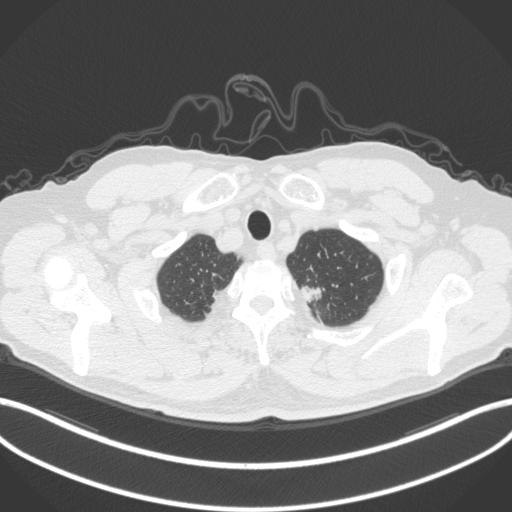
Chest CT, one axial slice; slice 349 of 382 in the series (ordered by position); reconstruction kernel B31f; lung window (W 1500 / L -600 HU); 1 mm slice thickness; 512 × 512 image matrix, field of view 400 × 400 mm. Patient: male, 64 years. Case-level facts recorded for this patient, not image findings: clinical TNM (as recorded): T1c N0 M0.
Structures marked on this image (bounding box drawn by a radiologist):
- lung tumour (recorded histology: adenocarcinoma): box from (x=298, y=278) to (x=327, y=307) px